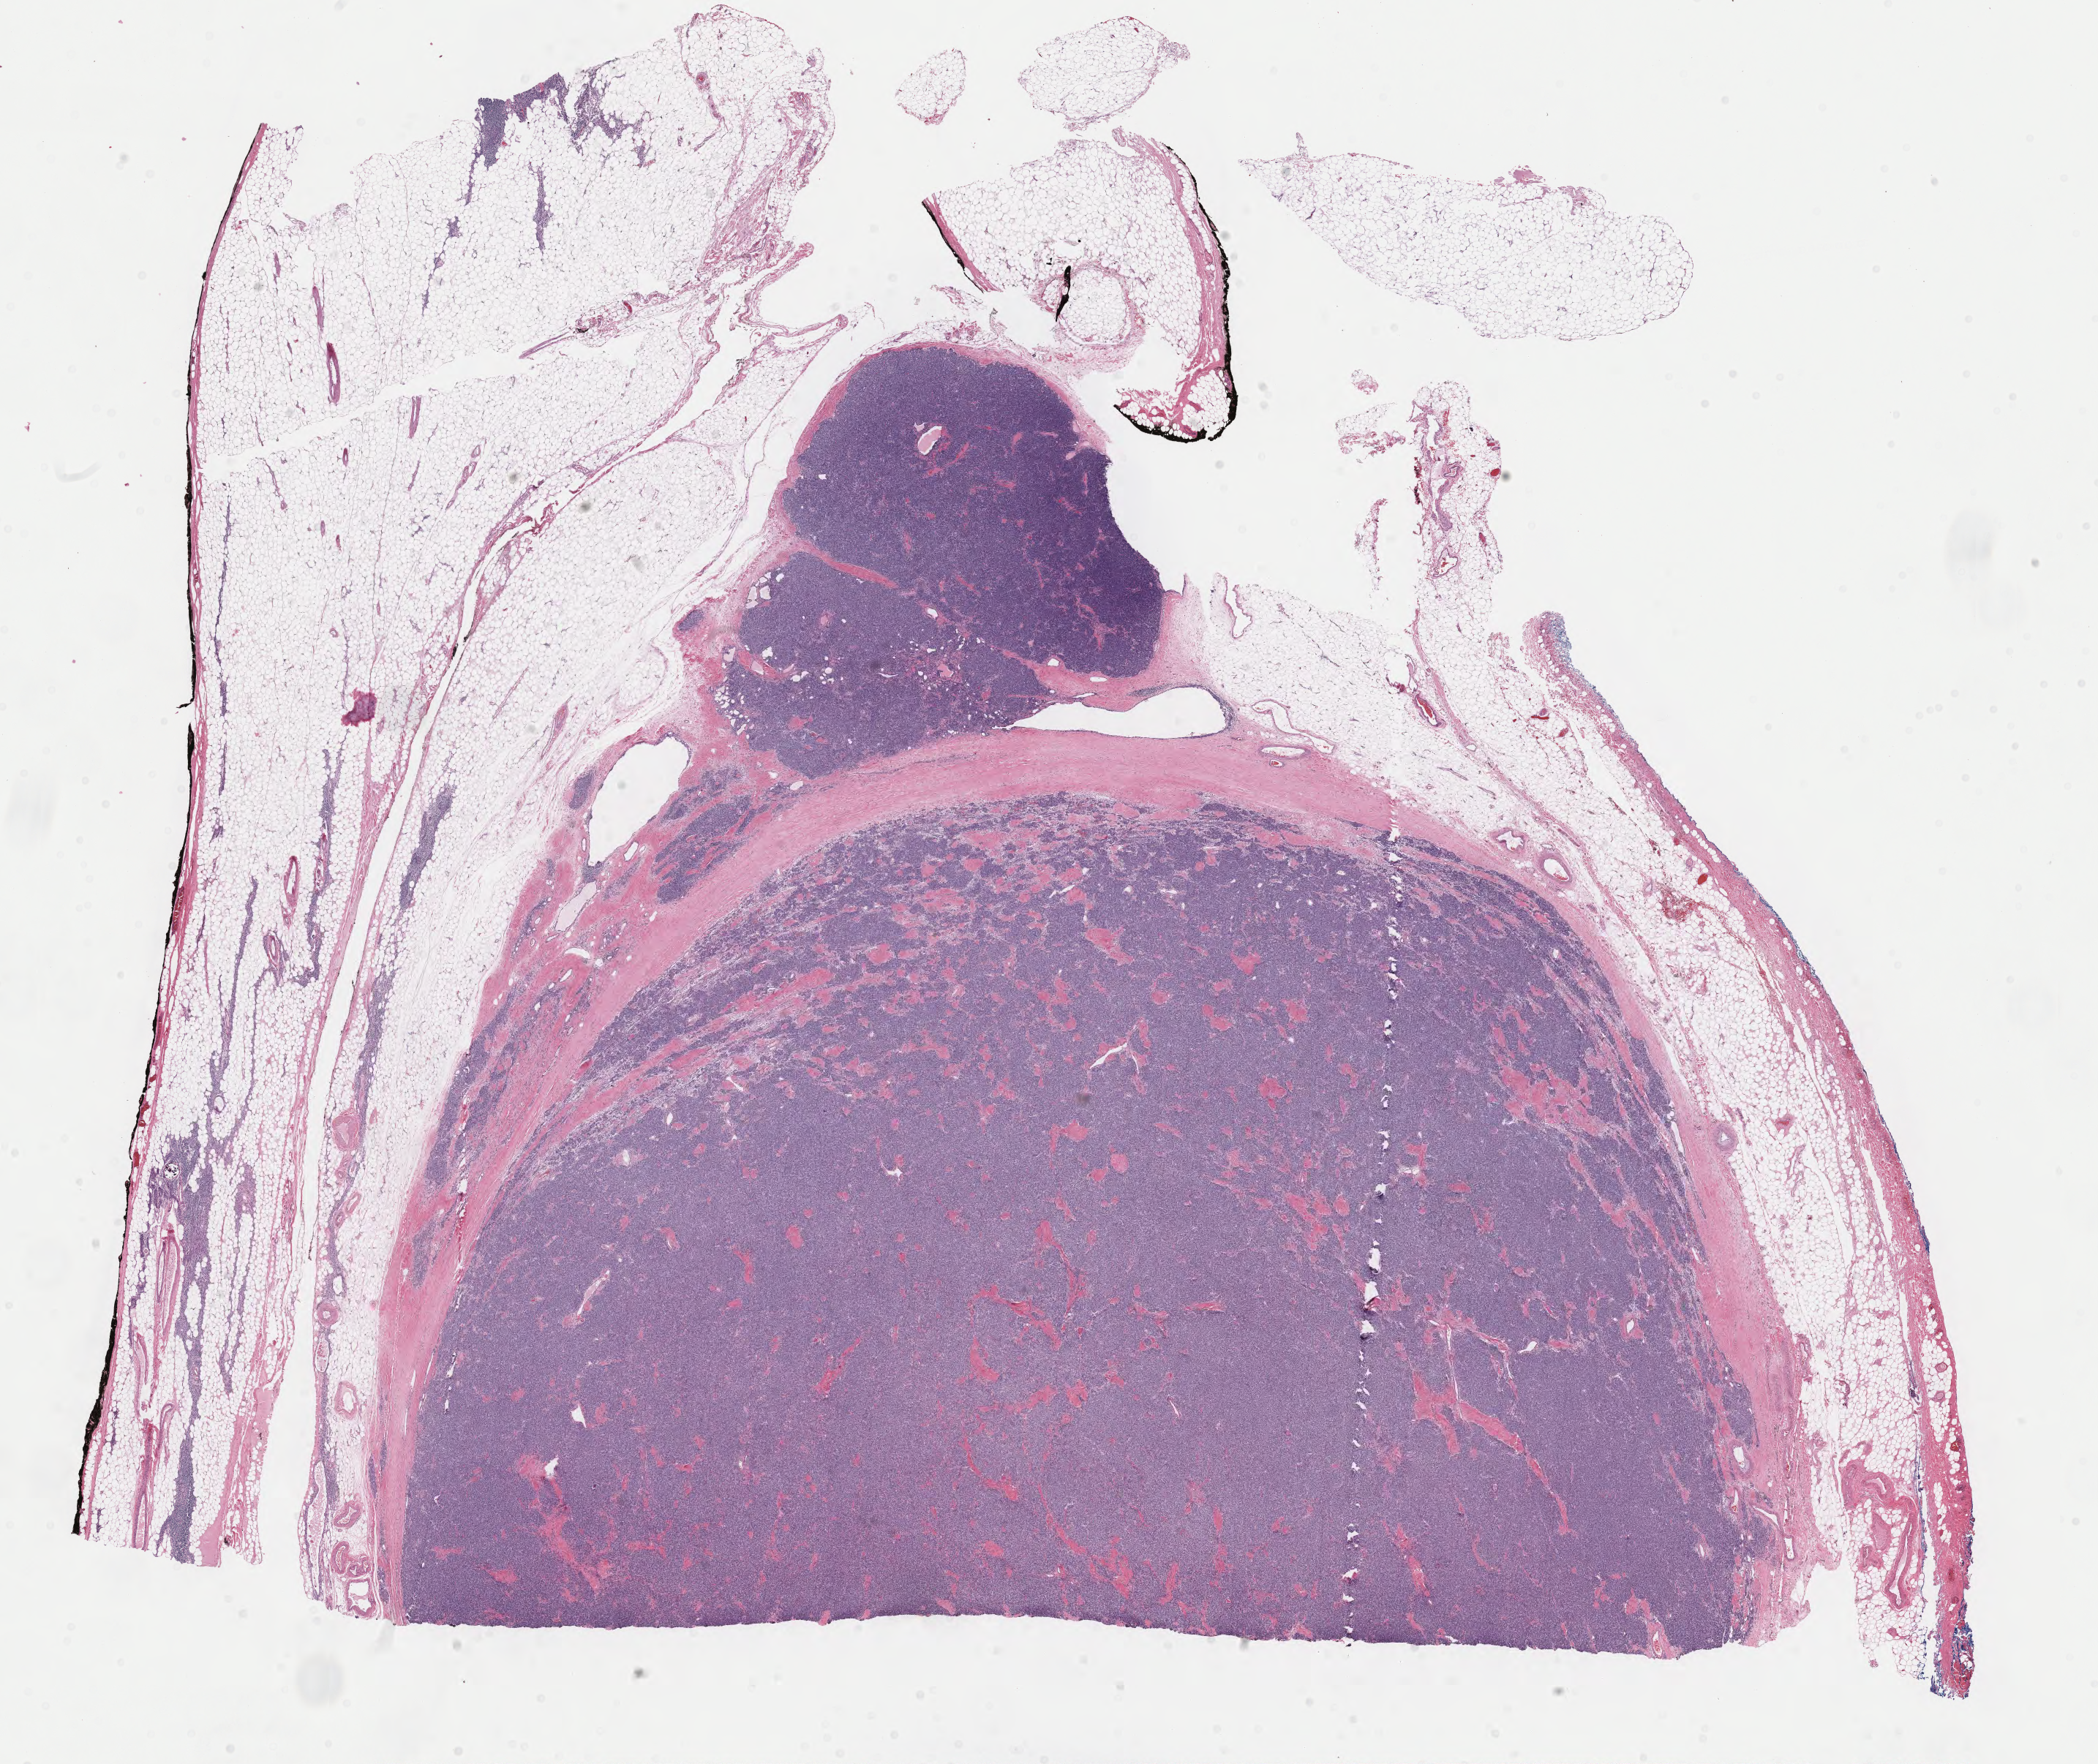
H&E whole-slide image, whole scanned area (about 22.7 x 19.1 mm, from a 40x scan) shown as a low-resolution overview; formalin-fixed paraffin-embedded (FFPE) diagnostic section; primary tumour sample from the thymus. Male patient; age at initial diagnosis 52 years.
Histologic diagnosis: Thymoma, type A, malignant.